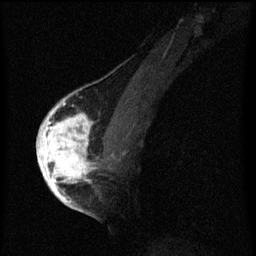
Breast MRI (dynamic contrast-enhanced), one sagittal slice. Slice 35 of 60 in the series (ordered by position). Dynamic contrast-enhanced series, image 2 of 3 at this slice position (ordered by acquisition). 1.5 T. TE 4.2 ms, TR 8 ms. 2 mm slice thickness. 256 × 256 image matrix, field of view 180 × 180 mm. Female patient, age 56 years.
Annotated regions visible in this slice (semi-automatic segmentation, software-assisted and operator-edited):
- analysis volume of interest (the breast-tissue region the enhancement analysis was run in; not a lesion): bounding box <42,110,99,193> (left, top, right, bottom; pixels)
- tumour enhancement mask (voxels above the 70 % enhancement threshold inside the analysis volume of interest): <42,110,97,193>